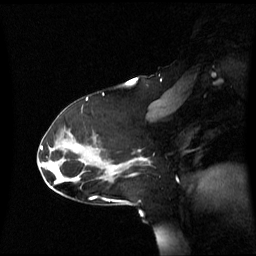
Breast MRI (dynamic contrast-enhanced), one sagittal slice; dynamic contrast-enhanced series, image 2 of 3 at this slice position (ordered by acquisition); 1.5 T; TE 4.2 ms, TR 8.4 ms; 256 × 256 image matrix, field of view 270 × 270 mm. Patient: female, 39 years. From the clinical record (not read from this slice): setting: breast cancer imaged before/during neoadjuvant chemotherapy; receptor status: triple-negative.
Outlined on this slice (semi-automatic segmentation, software-assisted and operator-edited):
- analysis volume of interest (the breast-tissue region the enhancement analysis was run in; not a lesion): bounding box (x1, y1, x2, y2) in pixels: (117, 157, 149, 174)
- tumour enhancement mask (voxels above the 70 % enhancement threshold inside the analysis volume of interest): (139, 158, 146, 161)